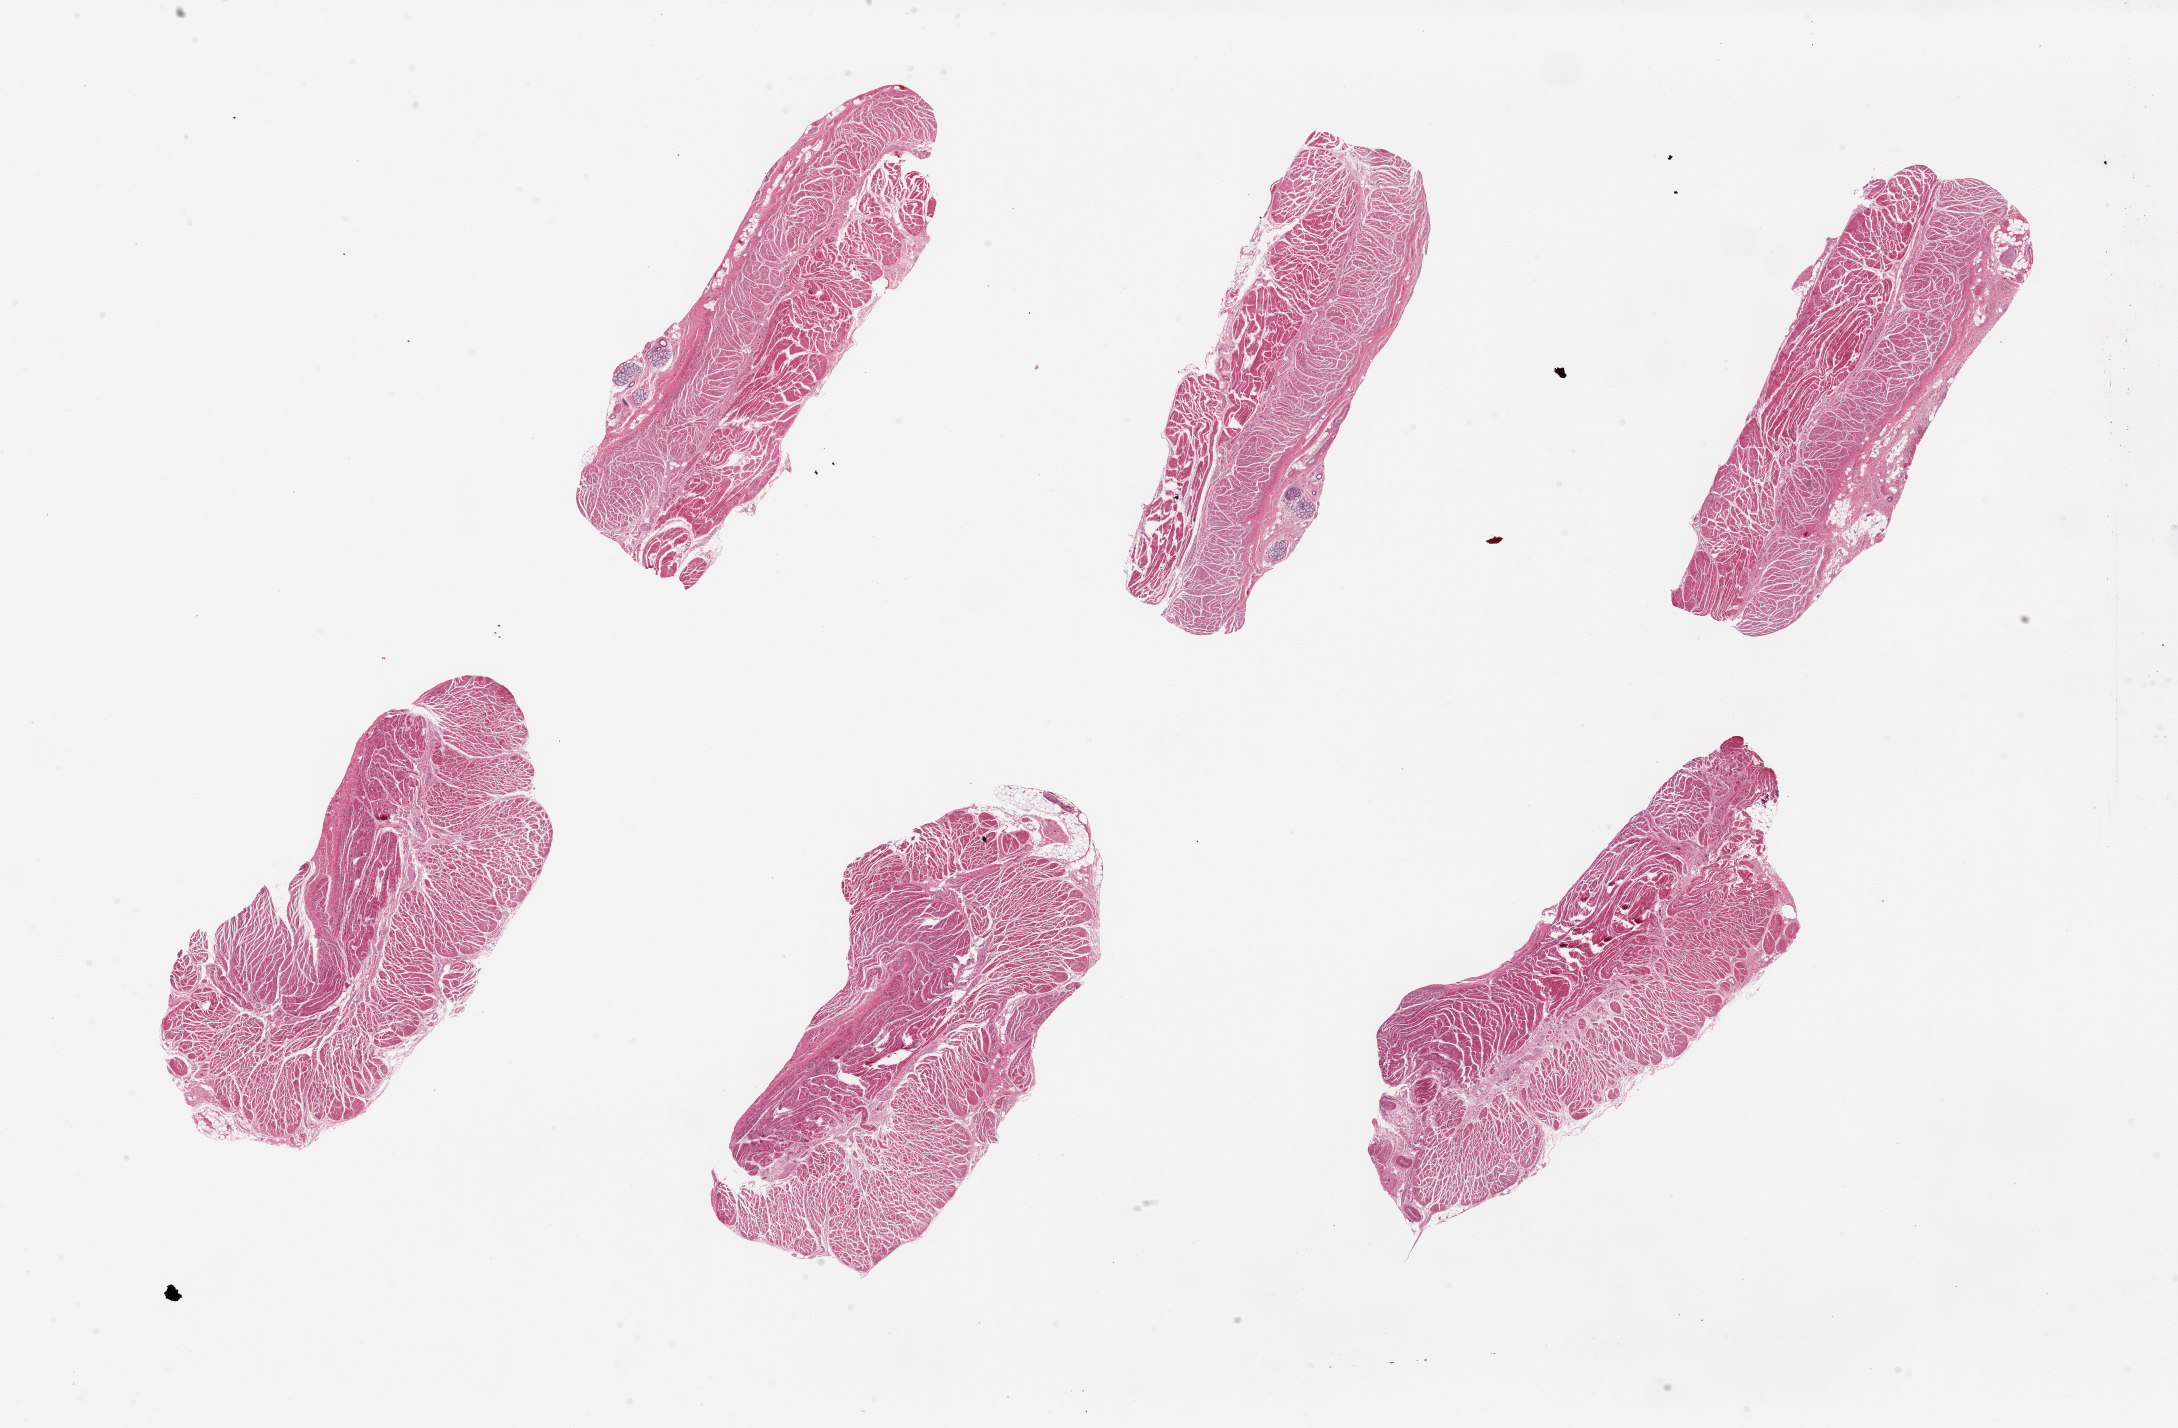
Digitized haematoxylin and eosin-stained section, shown as a low-resolution overview of the whole scanned area (about 34.5 x 22.6 mm); PAXgene-fixed, paraffin-embedded tissue; section of gastroesophageal junction (target tissue); donor tissue sample. Donor: female.
Review note (as recorded): 6 pieces, up to 9x3mm; all muscle, good specimens; Sub-mucosal mucinous glands noted in several sections.